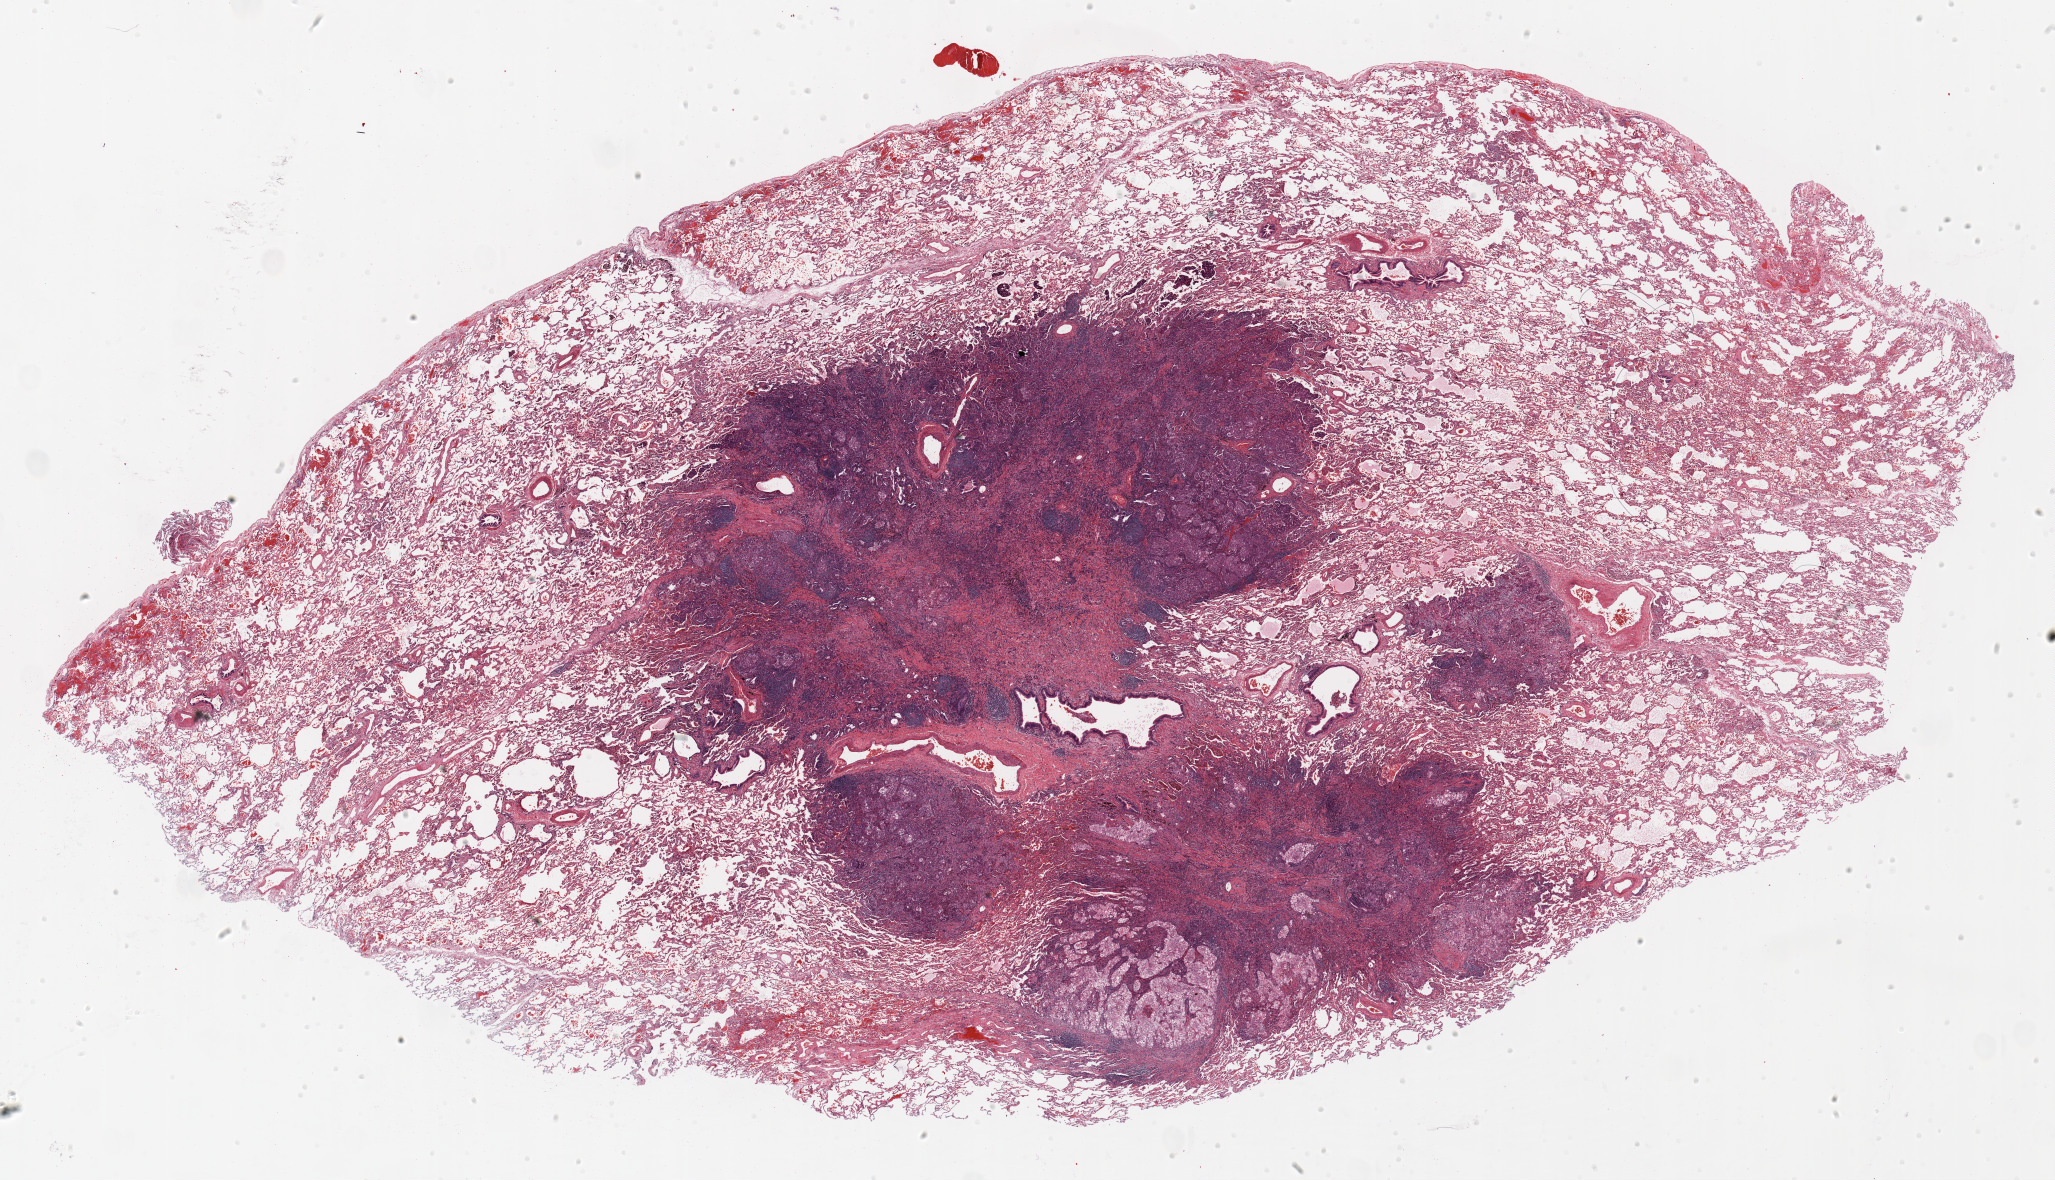
Whole-slide histology image, Hematoxylin and eosin (H&E) stained — shown as a low-resolution overview of the whole scanned area (about 33.0 x 19.0 mm). Formalin-fixed paraffin-embedded (FFPE) section. Lung tissue. Female, age 65 at enrolment. Current smoker at enrolment. Grade: poorly differentiated (G3).
Participant's lung-cancer diagnosis: Large cell carcinoma, NOS. Stage (AJCC 6th edition): IA. Primary tumour location (clinical record): right upper lobe. Tumour size (pathology): 20 mm. ICD-O-3 topography: upper lobe of lung (C34.1).